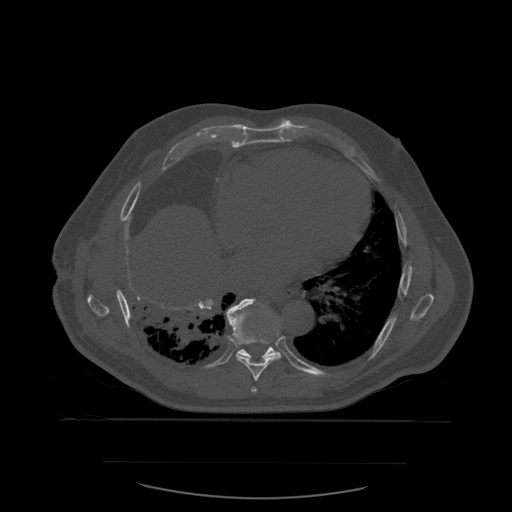
CT including the spine, one axial slice; slice 354 of 590 in the series (ordered by position); bone window (W 1800 / L 400 HU); 512 × 512 image matrix, field of view 479 × 479 mm. Patient age 71 years. Case-level facts recorded for this patient, not image findings: primary cancer: lung.
Structures marked on this image (semi-automatic segmentation, software-assisted and operator-edited):
- T7 vertebra: bounding box [x1, y1, x2, y2] px = [251, 387, 257, 393]
- T8 vertebra: [226, 300, 282, 382]
- T9 vertebra: [230, 299, 280, 360]